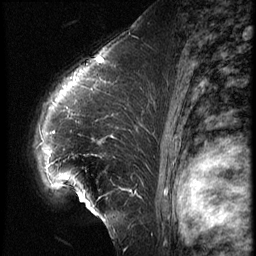
Breast MRI (dynamic contrast-enhanced), one sagittal slice. Position 43 of 62 along the scan axis. 3 images stored at this slice position (order not interpretable as contrast timing). 1.5 T. TE 4.2 ms, TR 9 ms. 2.5 mm slice thickness. 256 × 256 image matrix. Female patient, age 39 years. Case-level facts recorded for this patient, not image findings: setting: breast cancer imaged before/during neoadjuvant chemotherapy; receptor status: HER2-positive.
Outlined on this slice (semi-automatically segmented with operator editing):
- analysis volume of interest (the breast-tissue region the enhancement analysis was run in; not a lesion): bounding box [x1, y1, x2, y2] px = [29, 64, 153, 228]
- tumour enhancement mask (voxels above the 140 % enhancement threshold inside the analysis volume of interest): [53, 79, 113, 139]